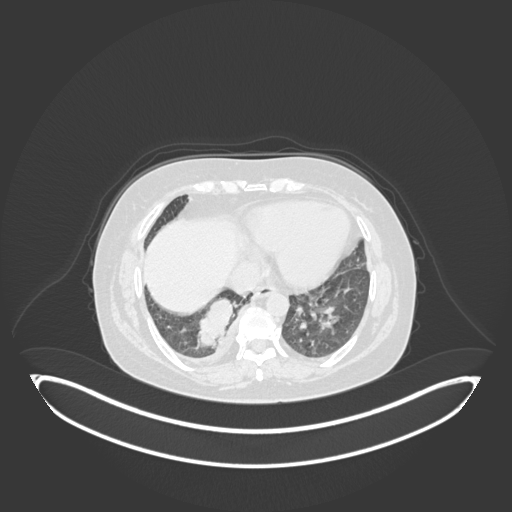
Chest CT, one axial slice. Position 41 of 231 along the scan axis. Lung window (W 1500 / L -600 HU). 1 mm slice thickness. 512 × 512 image matrix. Patient: female, 56 years. From the clinical record (not read from this slice): clinical TNM (as recorded): T2b N1 M0; histopathological grade: G3.
Structures marked on this image (rectangle marked by the reading radiologist):
- lung tumour (recorded histology: small cell carcinoma): bounding box (x1, y1, x2, y2) in pixels: (191, 290, 239, 351)